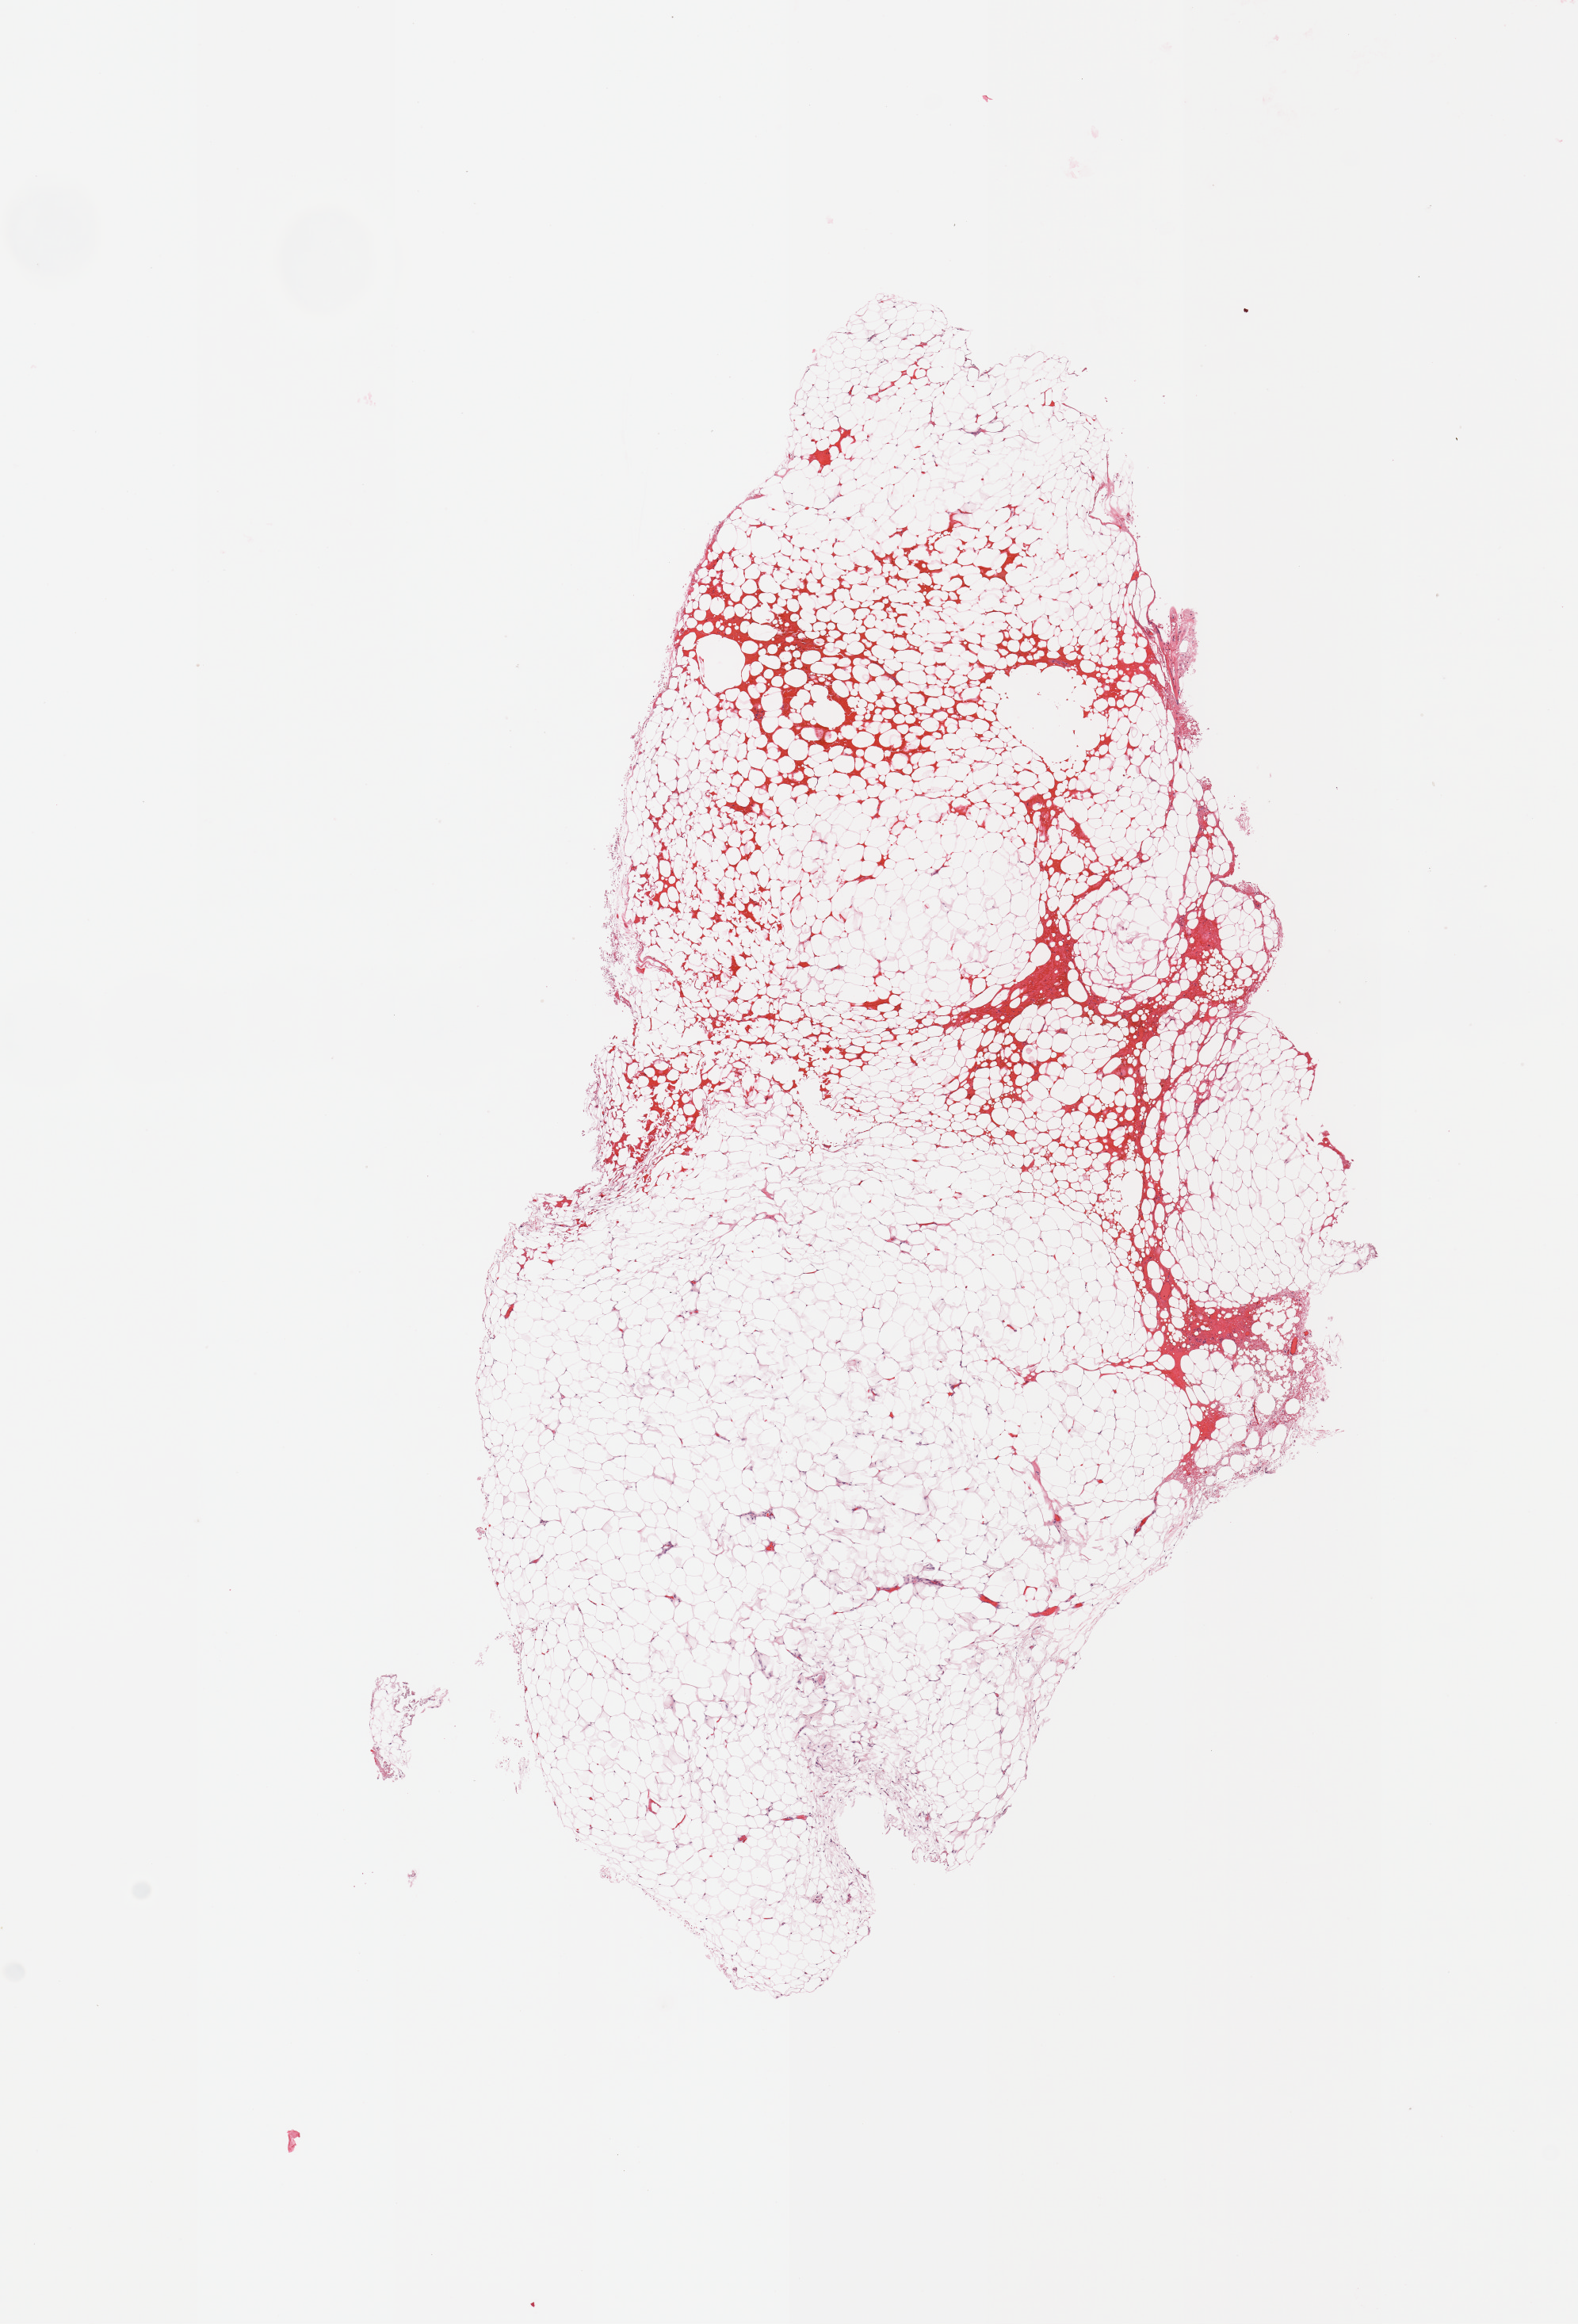
Hematoxylin and eosin (H&E) stained whole-slide image, whole scanned area (about 7.9 x 11.6 mm) shown as a low-resolution overview. Kidney, normal (non-tumour) tissue. Female patient, aged 90 or older.
• this section: normal (non-tumour) tissue from the same patient
• patient diagnosis: Renal cell carcinoma, NOS